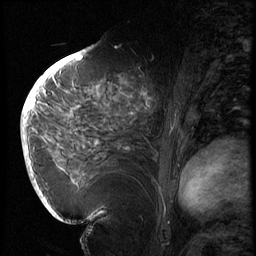
Breast MRI (dynamic contrast-enhanced), one sagittal slice; position 36 of 72 along the scan axis; 3 images stored at this slice position (order not interpretable as contrast timing); 1.5 T; TE 4.2 ms, TR 8.9 ms; 2.5 mm slice thickness; 256 × 256 image matrix, field of view 200 × 200 mm. Female patient, age 56 years. Case-level facts recorded for this patient, not image findings: setting: breast cancer imaged before/during neoadjuvant chemotherapy.
Outlined on this slice (semi-automatically segmented with operator editing):
- analysis volume of interest (the breast-tissue region the enhancement analysis was run in; not a lesion): bounding box (x1, y1, x2, y2) in pixels: (114, 76, 177, 138)
- tumour enhancement mask (voxels above the 140 % enhancement threshold inside the analysis volume of interest): (141, 94, 150, 109)